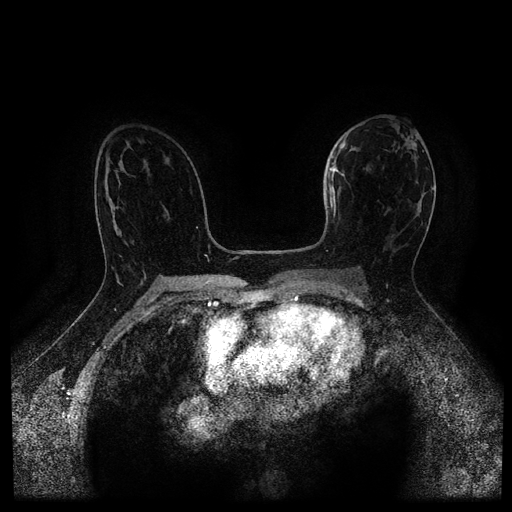
Breast MRI (dynamic contrast-enhanced, multi-phase), one axial slice. Slice 60 of 116 in the series (ordered by position). Dynamic contrast-enhanced series, time point 2 of 5 at this slice position (early post-contrast). 1.5 T. TE 2.7 ms, TR 5.4 ms. 2 mm slice thickness. 512 × 512 image matrix. Patient: female, 50 years.
Structures marked on this image (semi-automatically segmented with operator editing):
- breast lesion (labelled 'tumour' in the annotation; benign lesions carry a separate 'benign' label): box from (x=328, y=166) to (x=336, y=218) px